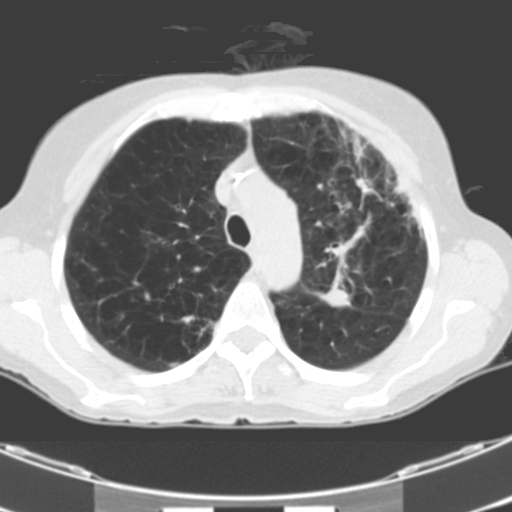
Low-dose screening chest CT, one axial slice; position 80 of 106 along the scan axis; 120 kVp; one of 2 acquisitions stored at this slice position; lung window (W 1500 / L -600 HU); 3.2 mm slice thickness; 512 × 512 image matrix, field of view 299 × 299 mm.
Structures marked on this image (outlined manually by an expert reader):
- lesion 1 (tumor): bounding box [x1, y1, x2, y2] px = [320, 291, 351, 307]